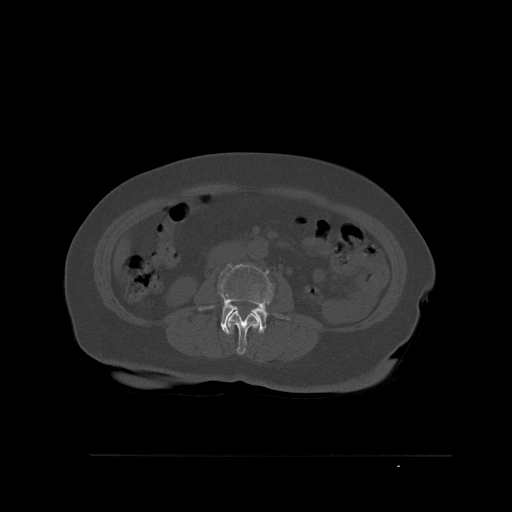
CT including the spine, one axial slice; slice 234 of 527 in the series (ordered by position); bone window (W 1800 / L 400 HU); 1.5 mm slice thickness; 512 × 512 image matrix, field of view 470 × 470 mm. Female patient, age 73 years. From the clinical record (not read from this slice): primary cancer: breast; vertebrae with lytic lesions (as recorded): L2.
Structures marked on this image (semi-automatic segmentation, software-assisted and operator-edited):
- L2 vertebra: bounding box (x1, y1, x2, y2) in pixels: (226, 310, 257, 355)
- L3 vertebra: (198, 263, 290, 335)
- L4 vertebra: (253, 320, 259, 332)